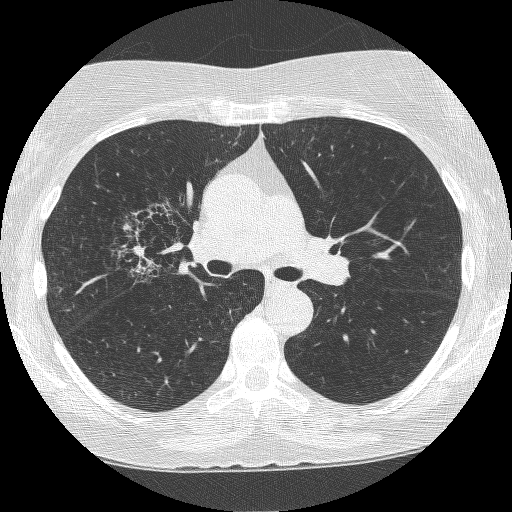
Axial slice from a low-dose chest CT screening exam, second annual screen, lung window (W 1500 / L -600 HU), 1.25 mm slice thickness, lung (sharp) reconstruction kernel (BONE), slice 149 of 249 in the series, 512 × 512 image matrix, field of view 308 × 308 mm. Female, age 64 years at enrolment.
Expert-annotated lung lesion, bounding box [x1, y1, x2, y2] px = [116, 205, 204, 289]. The screening reader recorded 4 non-calcified nodules or masses ≥4 mm on this exam (right upper lobe, right upper lobe, right upper lobe, left upper lobe); which of them this box marks is not recorded. Lung cancer was diagnosed 381 days after this screen: adenocarcinoma, NOS, right upper lobe, right middle lobe, right hilum, stage IV (AJCC 6th edition), 85 mm at pathology.